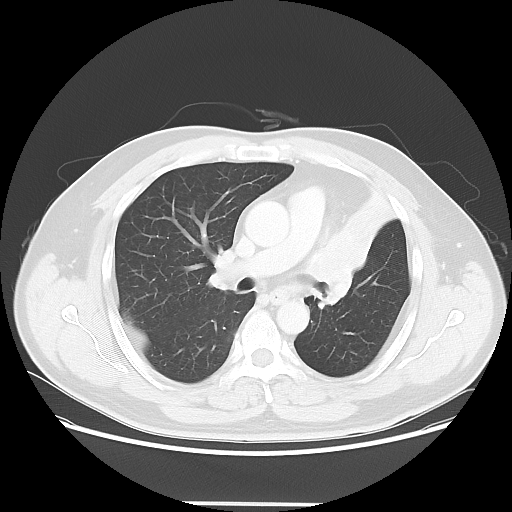
Chest CT, one axial slice; position 37 of 62 along the scan axis; reconstruction kernel LUNG; lung window (W 1500 / L -600 HU); 5 mm slice thickness; 512 × 512 image matrix, field of view 403 × 403 mm. Patient: male, 49 years. Case-level facts recorded for this patient, not image findings: clinical TNM (as recorded): T3 N3 M1c.
Outlined on this slice (rectangle marked by the reading radiologist):
- lung tumour (recorded histology: squamous cell carcinoma): bounding box [x1, y1, x2, y2] px = [308, 226, 384, 306]